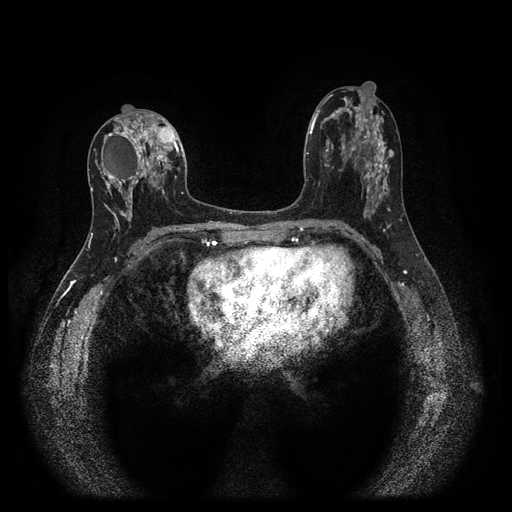
Breast MRI (dynamic contrast-enhanced, multi-phase), one axial slice. Position 51 of 116 along the scan axis. Dynamic contrast-enhanced series, time point 2 of 5 at this slice position (early post-contrast). 1.5 T. TE 2.7 ms, TR 5.4 ms. 512 × 512 image matrix, field of view 330 × 330 mm. Patient: female, 47 years.
Annotated regions visible in this slice (semi-automatically segmented with operator editing):
- breast lesion (labelled benign in the annotation): bounding box [x1, y1, x2, y2] px = [388, 149, 395, 159]
- breast lesion (labelled 'tumour' in the annotation; benign lesions carry a separate 'benign' label): [92, 116, 179, 226]